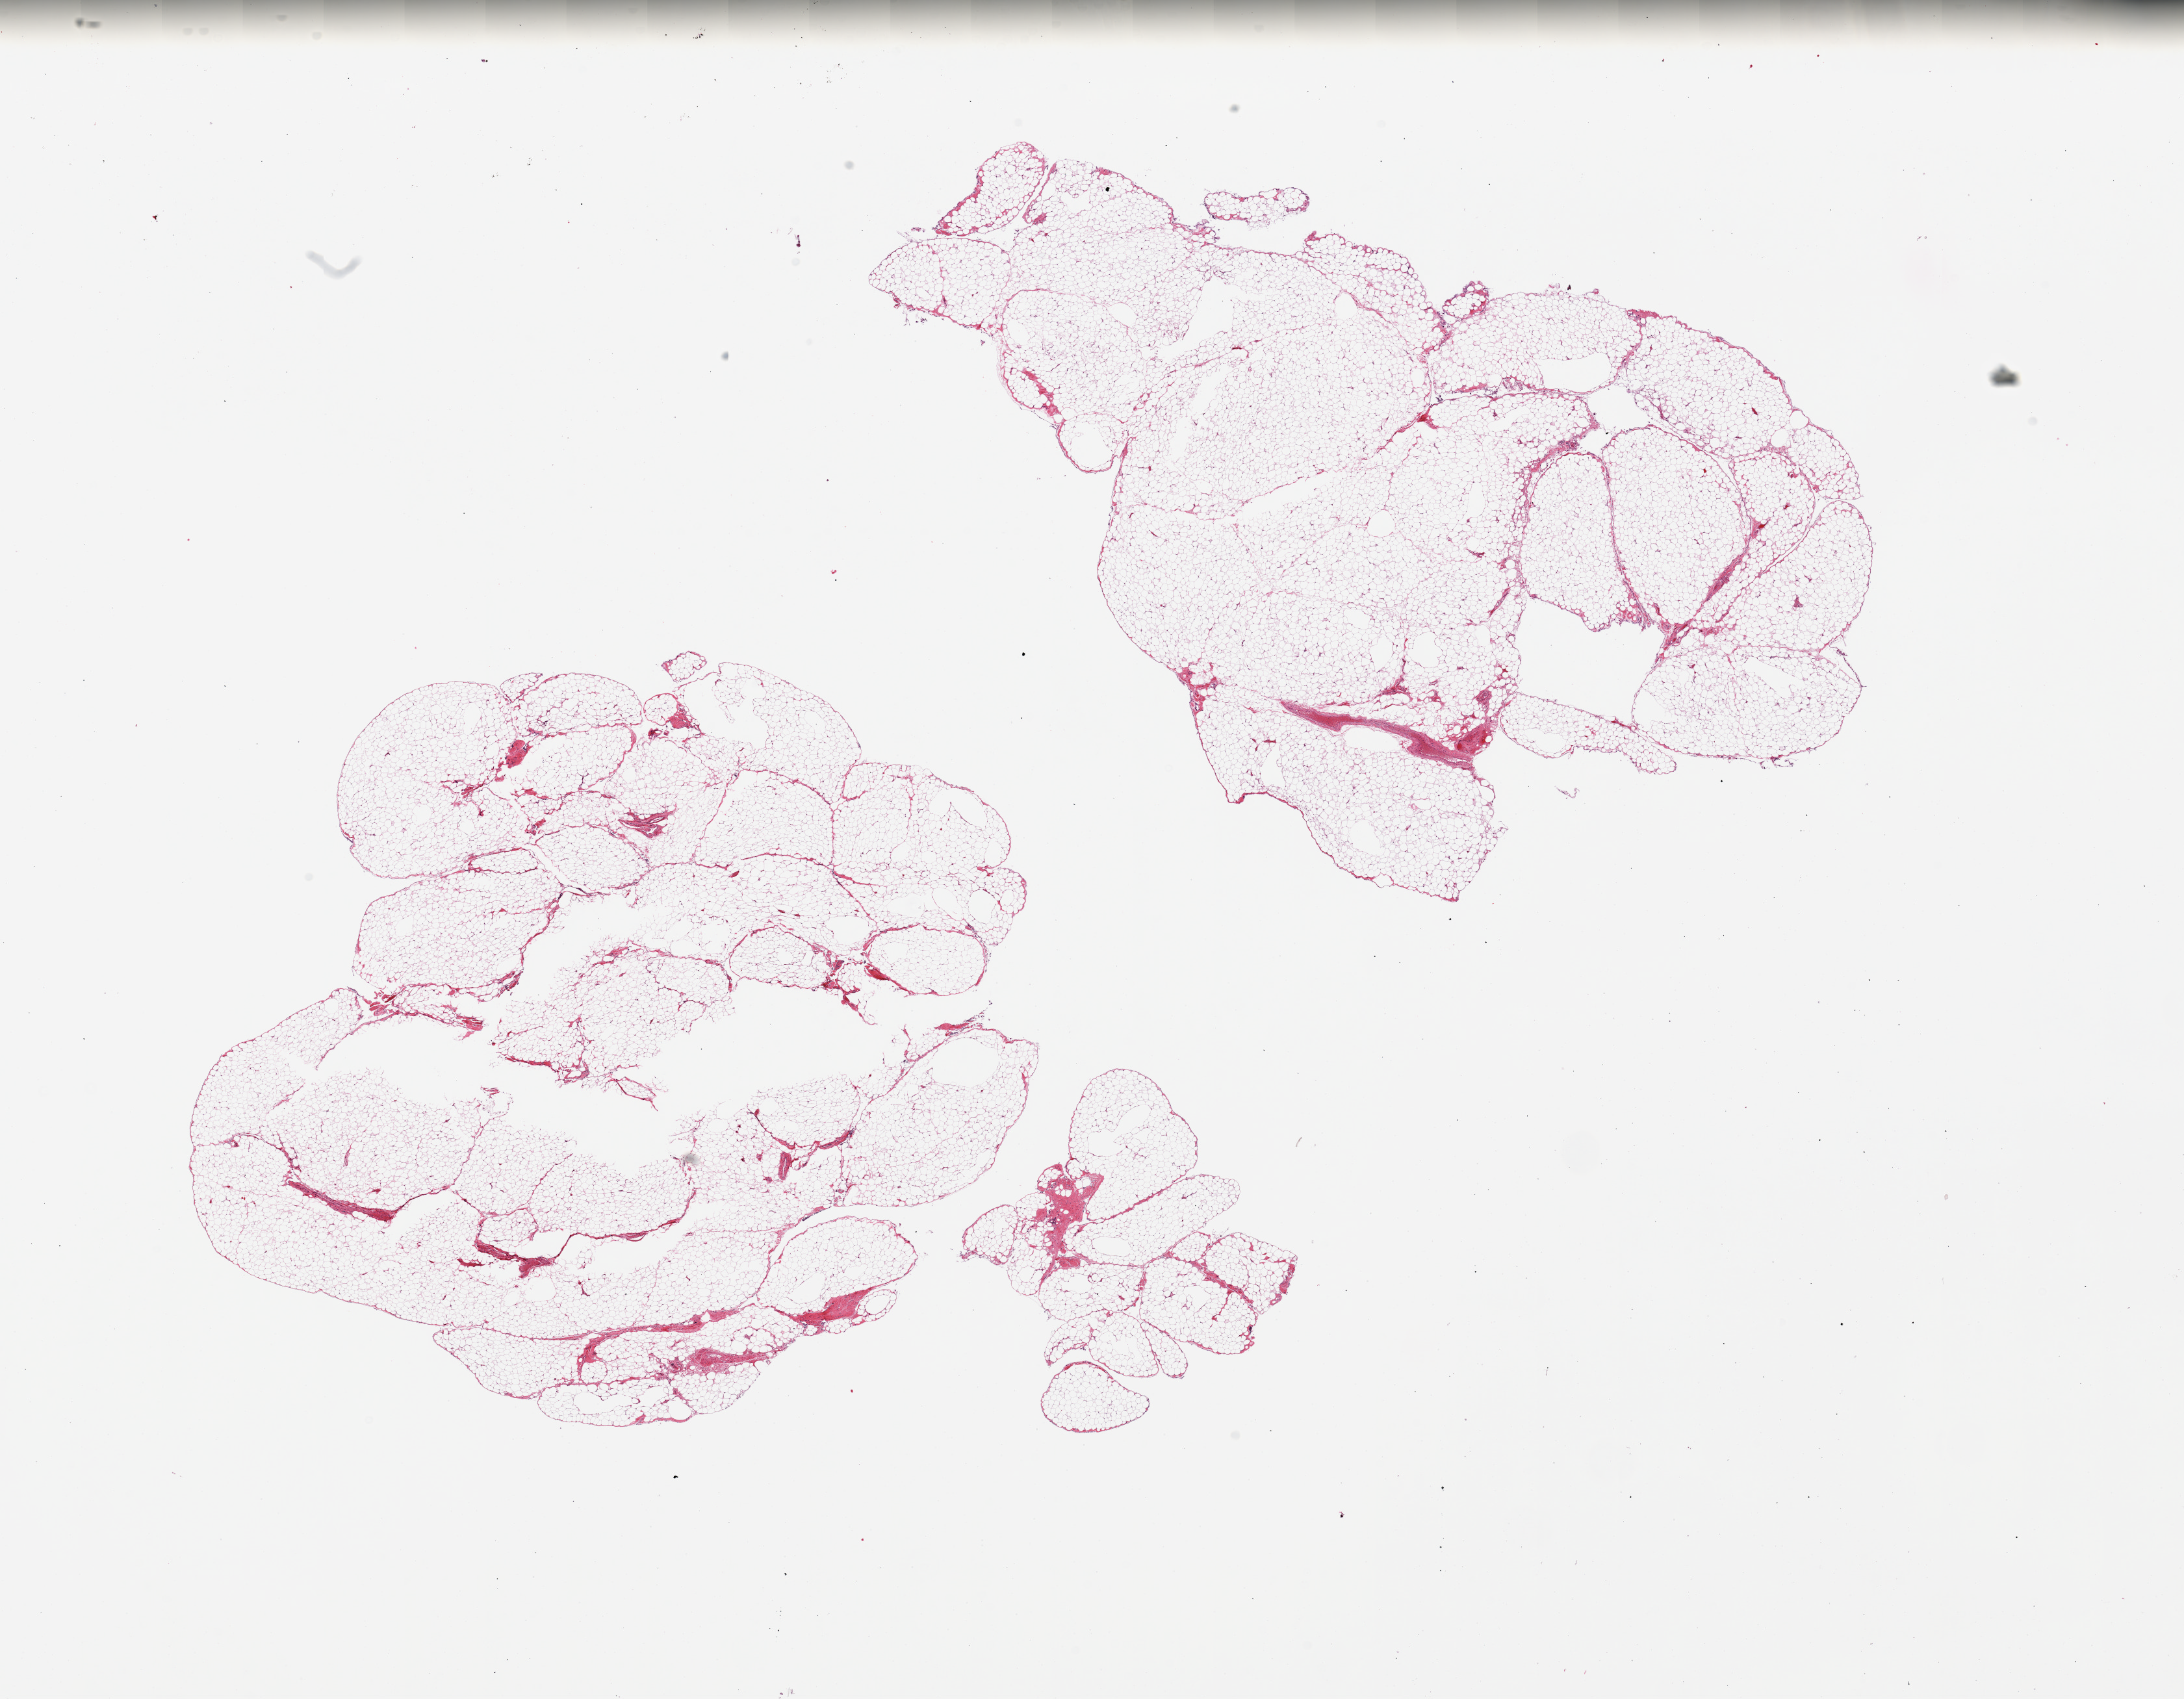
Whole-slide image, haematoxylin and eosin stain, low-resolution overview of the scanned area, about 26.6 x 20.7 mm; PAXgene-fixed paraffin-embedded (PFPE) section; target tissue: omentum; tissue donor sample. Donor sex: female.
Reviewer comment on this tissue sample: 2 pieces, minimal fibrous tissue.